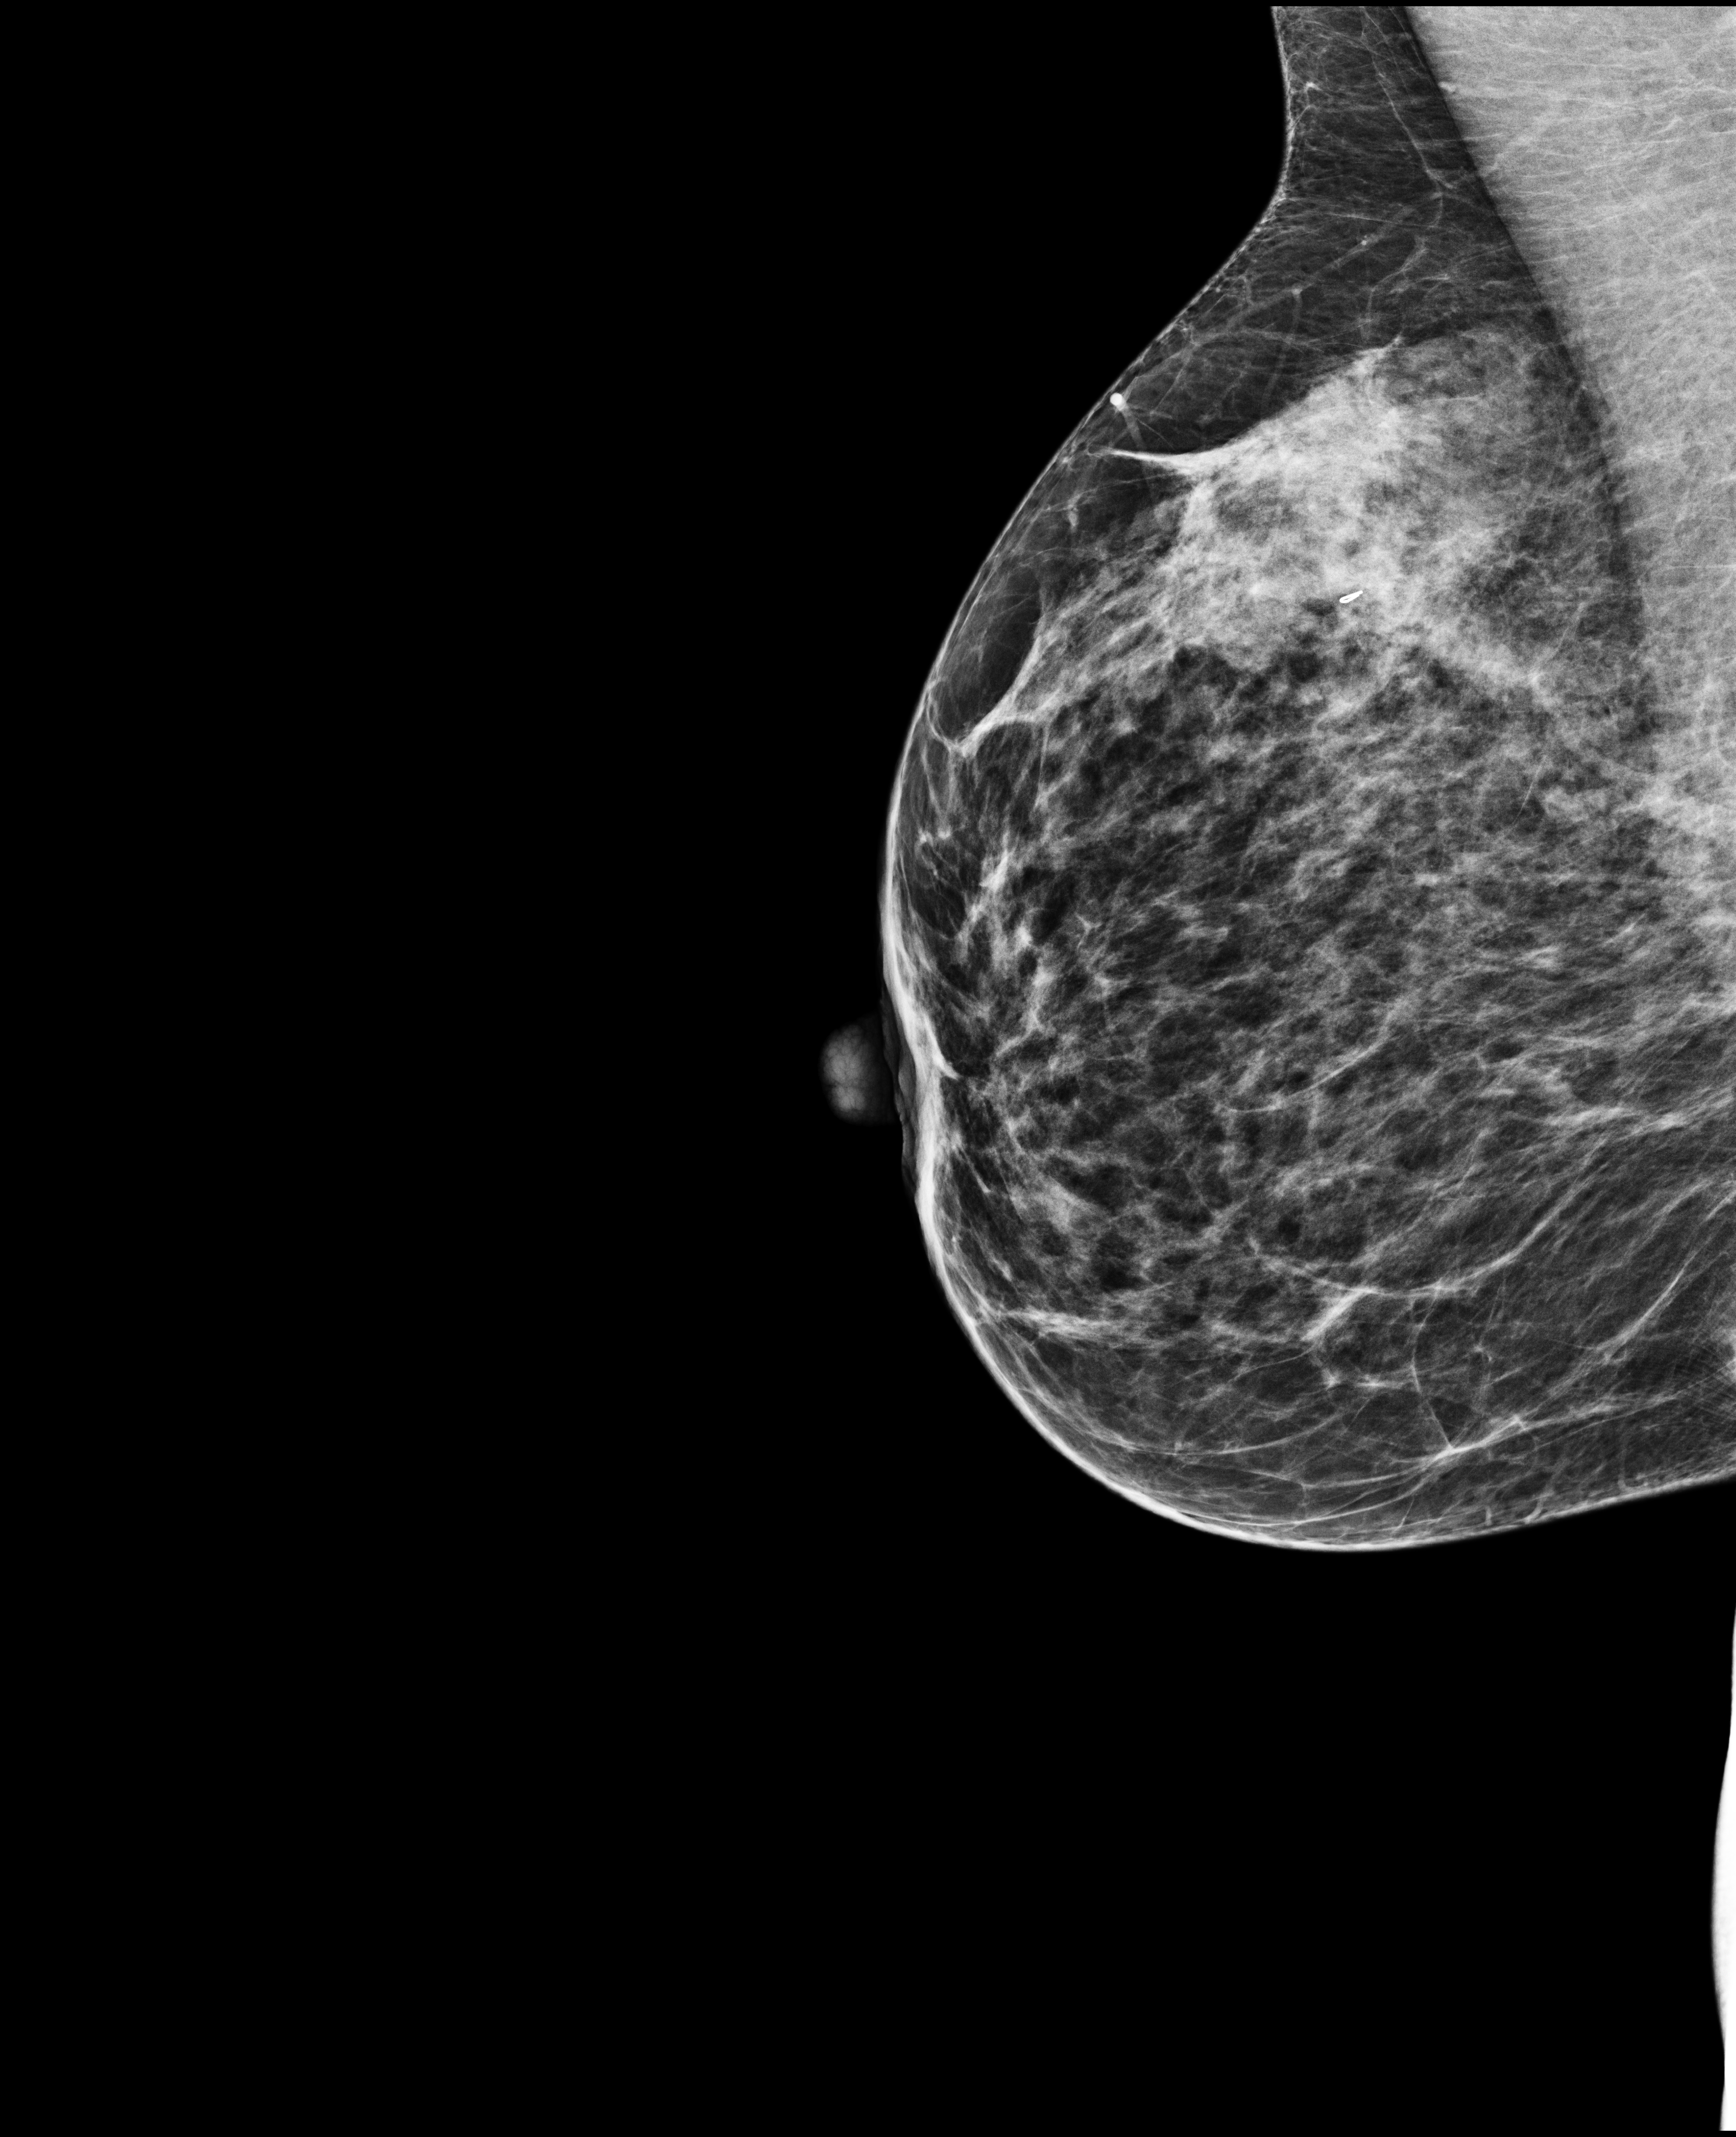
Screening examination; compressed breast thickness 54 mm.
Image type: full-field digital mammogram. Breast: right. Projection: mediolateral oblique (MLO) view.